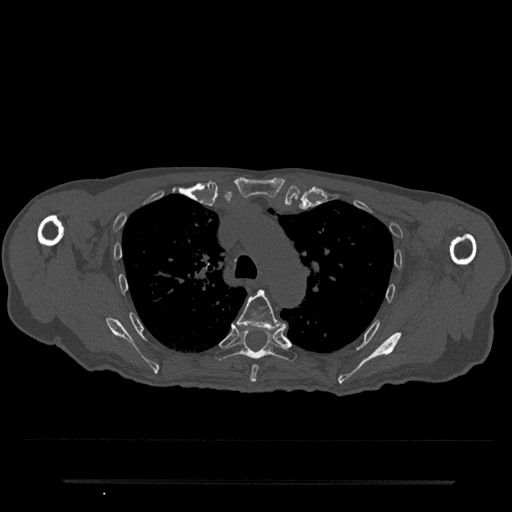
CT including the spine, one axial slice; position 553 of 797 along the scan axis; reconstruction kernel Br40s/3; 120 kVp; bone window (W 1800 / L 400 HU); 0.5 mm slice thickness; 512 × 512 image matrix, field of view 427 × 427 mm. Patient: male, 74 years. From the clinical record (not read from this slice): primary cancer: prostate.
Structures marked on this image (semi-automatic segmentation, software-assisted and operator-edited):
- T5 vertebra: bounding box [x1, y1, x2, y2] px = [236, 290, 287, 382]
- T6 vertebra: [214, 329, 297, 362]